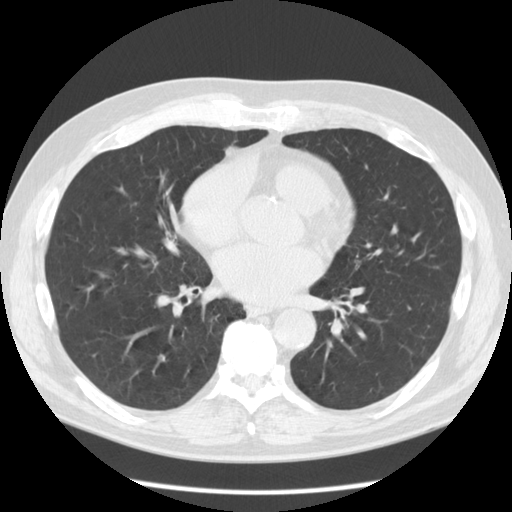
Chest CT (low-dose screening protocol), one axial image. Second screening round (one year after baseline). Lung window (W 1500 / L -600 HU). 2.5 mm slice thickness. Standard (soft-tissue) reconstruction kernel (STANDARD). Slice 74 of 133 in the series. 512 × 512 image matrix, field of view 360 × 360 mm. Male participant, aged 60 years at enrolment. Former smoker at enrolment.
• Expert reader's lesion annotation, bounding box (x1, y1, x2, y2) in pixels: (145, 343, 178, 376).
• Screening reader's record for this exam: no non-calcified nodule ≥4 mm recorded.
• Official screen result: negative screen, minor abnormalities not suspicious for lung cancer.
• Participant outcome: lung cancer diagnosed 689 days after this screen (after the third annual screen) — squamous cell carcinoma, clear cell type, right lower lobe, stage IV (AJCC 6th edition), 12 mm at pathology.